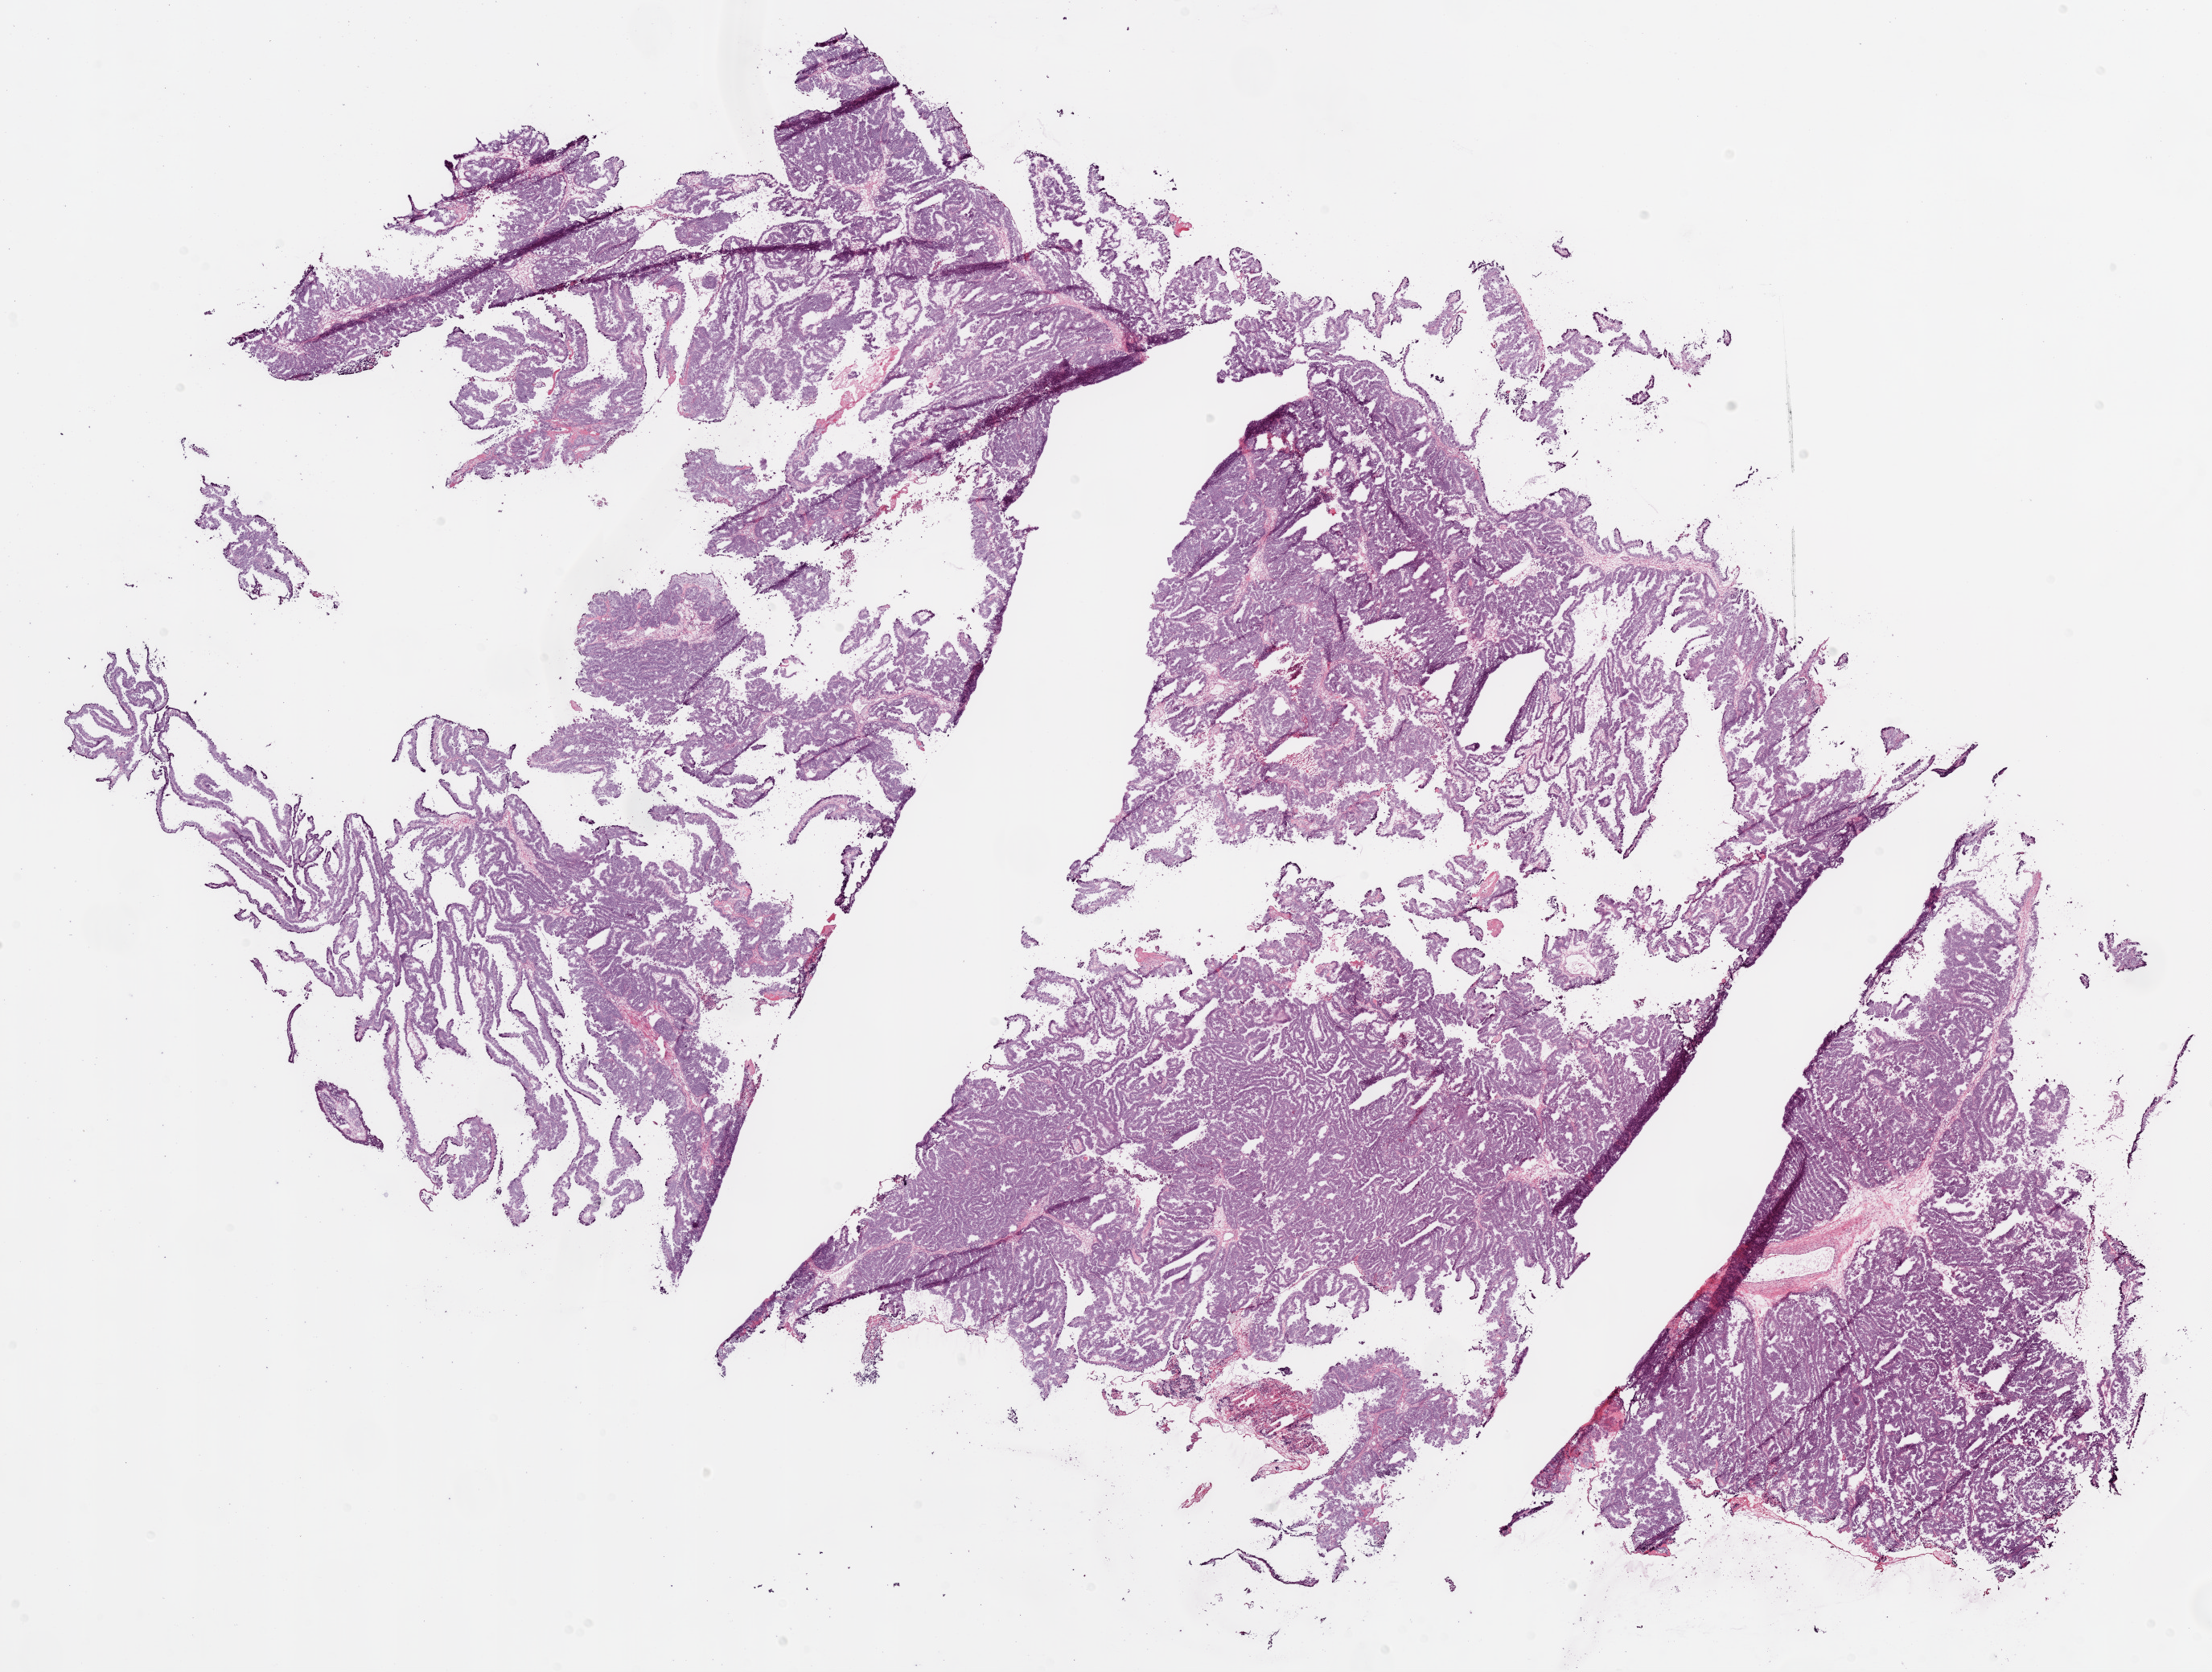
H&E-stained whole-slide image — whole scanned area (about 22.1 x 16.7 mm) shown as a low-resolution overview, frozen section, primary tumour sample from the ovary. Patient: female, age at initial diagnosis 79 years. Histologic grade: G3 (poorly differentiated). Composition of this section per pathologist review: tumour cells 90%, tumour nuclei 99%, normal cells 0%, stromal cells 5%, necrosis 5%.
FIGO stage: IIIC. Laterality: bilateral. Histologic diagnosis: Serous cystadenocarcinoma, NOS.